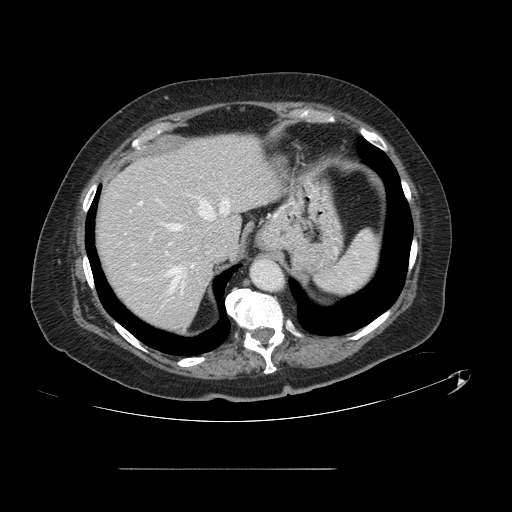
Contrast-enhanced abdominal CT, one axial slice. Position 108 of 148 along the scan axis. 120 kVp. Intravenous contrast given. Soft-tissue window (W 400 / L 40 HU). 2.5 mm slice thickness. 512 × 512 image matrix, field of view 439 × 439 mm. Female patient, age 75 years. From the clinical record (not read from this slice): diagnosis: colorectal cancer liver metastases, imaged before liver resection; multiple liver metastases: no; largest metastasis: 2.4 cm; disease in both lobes: no.
Outlined on this slice (outlined manually by an expert reader):
- hepatic veins: bounding box (x1, y1, x2, y2) in pixels: (168, 197, 230, 290)
- liver: (95, 135, 276, 330)
- planned liver remnant (the part of the liver to remain after resection): (95, 135, 276, 330)
- portal vein (with intrahepatic branches): (140, 202, 142, 205)